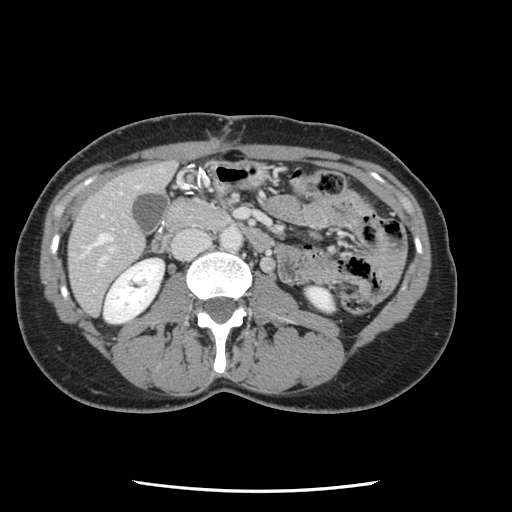
Contrast-enhanced abdominal CT, one axial slice. Slice 31 of 134 in the series (ordered by position). Intravenous contrast given. Soft-tissue window (W 400 / L 40 HU). 2.5 mm slice thickness. 512 × 512 image matrix. Female patient, age 43 years. Case-level facts recorded for this patient, not image findings: diagnosis: colorectal cancer liver metastases, imaged before liver resection; multiple liver metastases: yes; largest metastasis: 3.4 cm.
Structures marked on this image (outlined manually by an expert reader):
- hepatic veins: bounding box (x1, y1, x2, y2) in pixels: (95, 234, 111, 244)
- liver: (69, 163, 175, 315)
- planned liver remnant (the part of the liver to remain after resection): (69, 163, 175, 315)